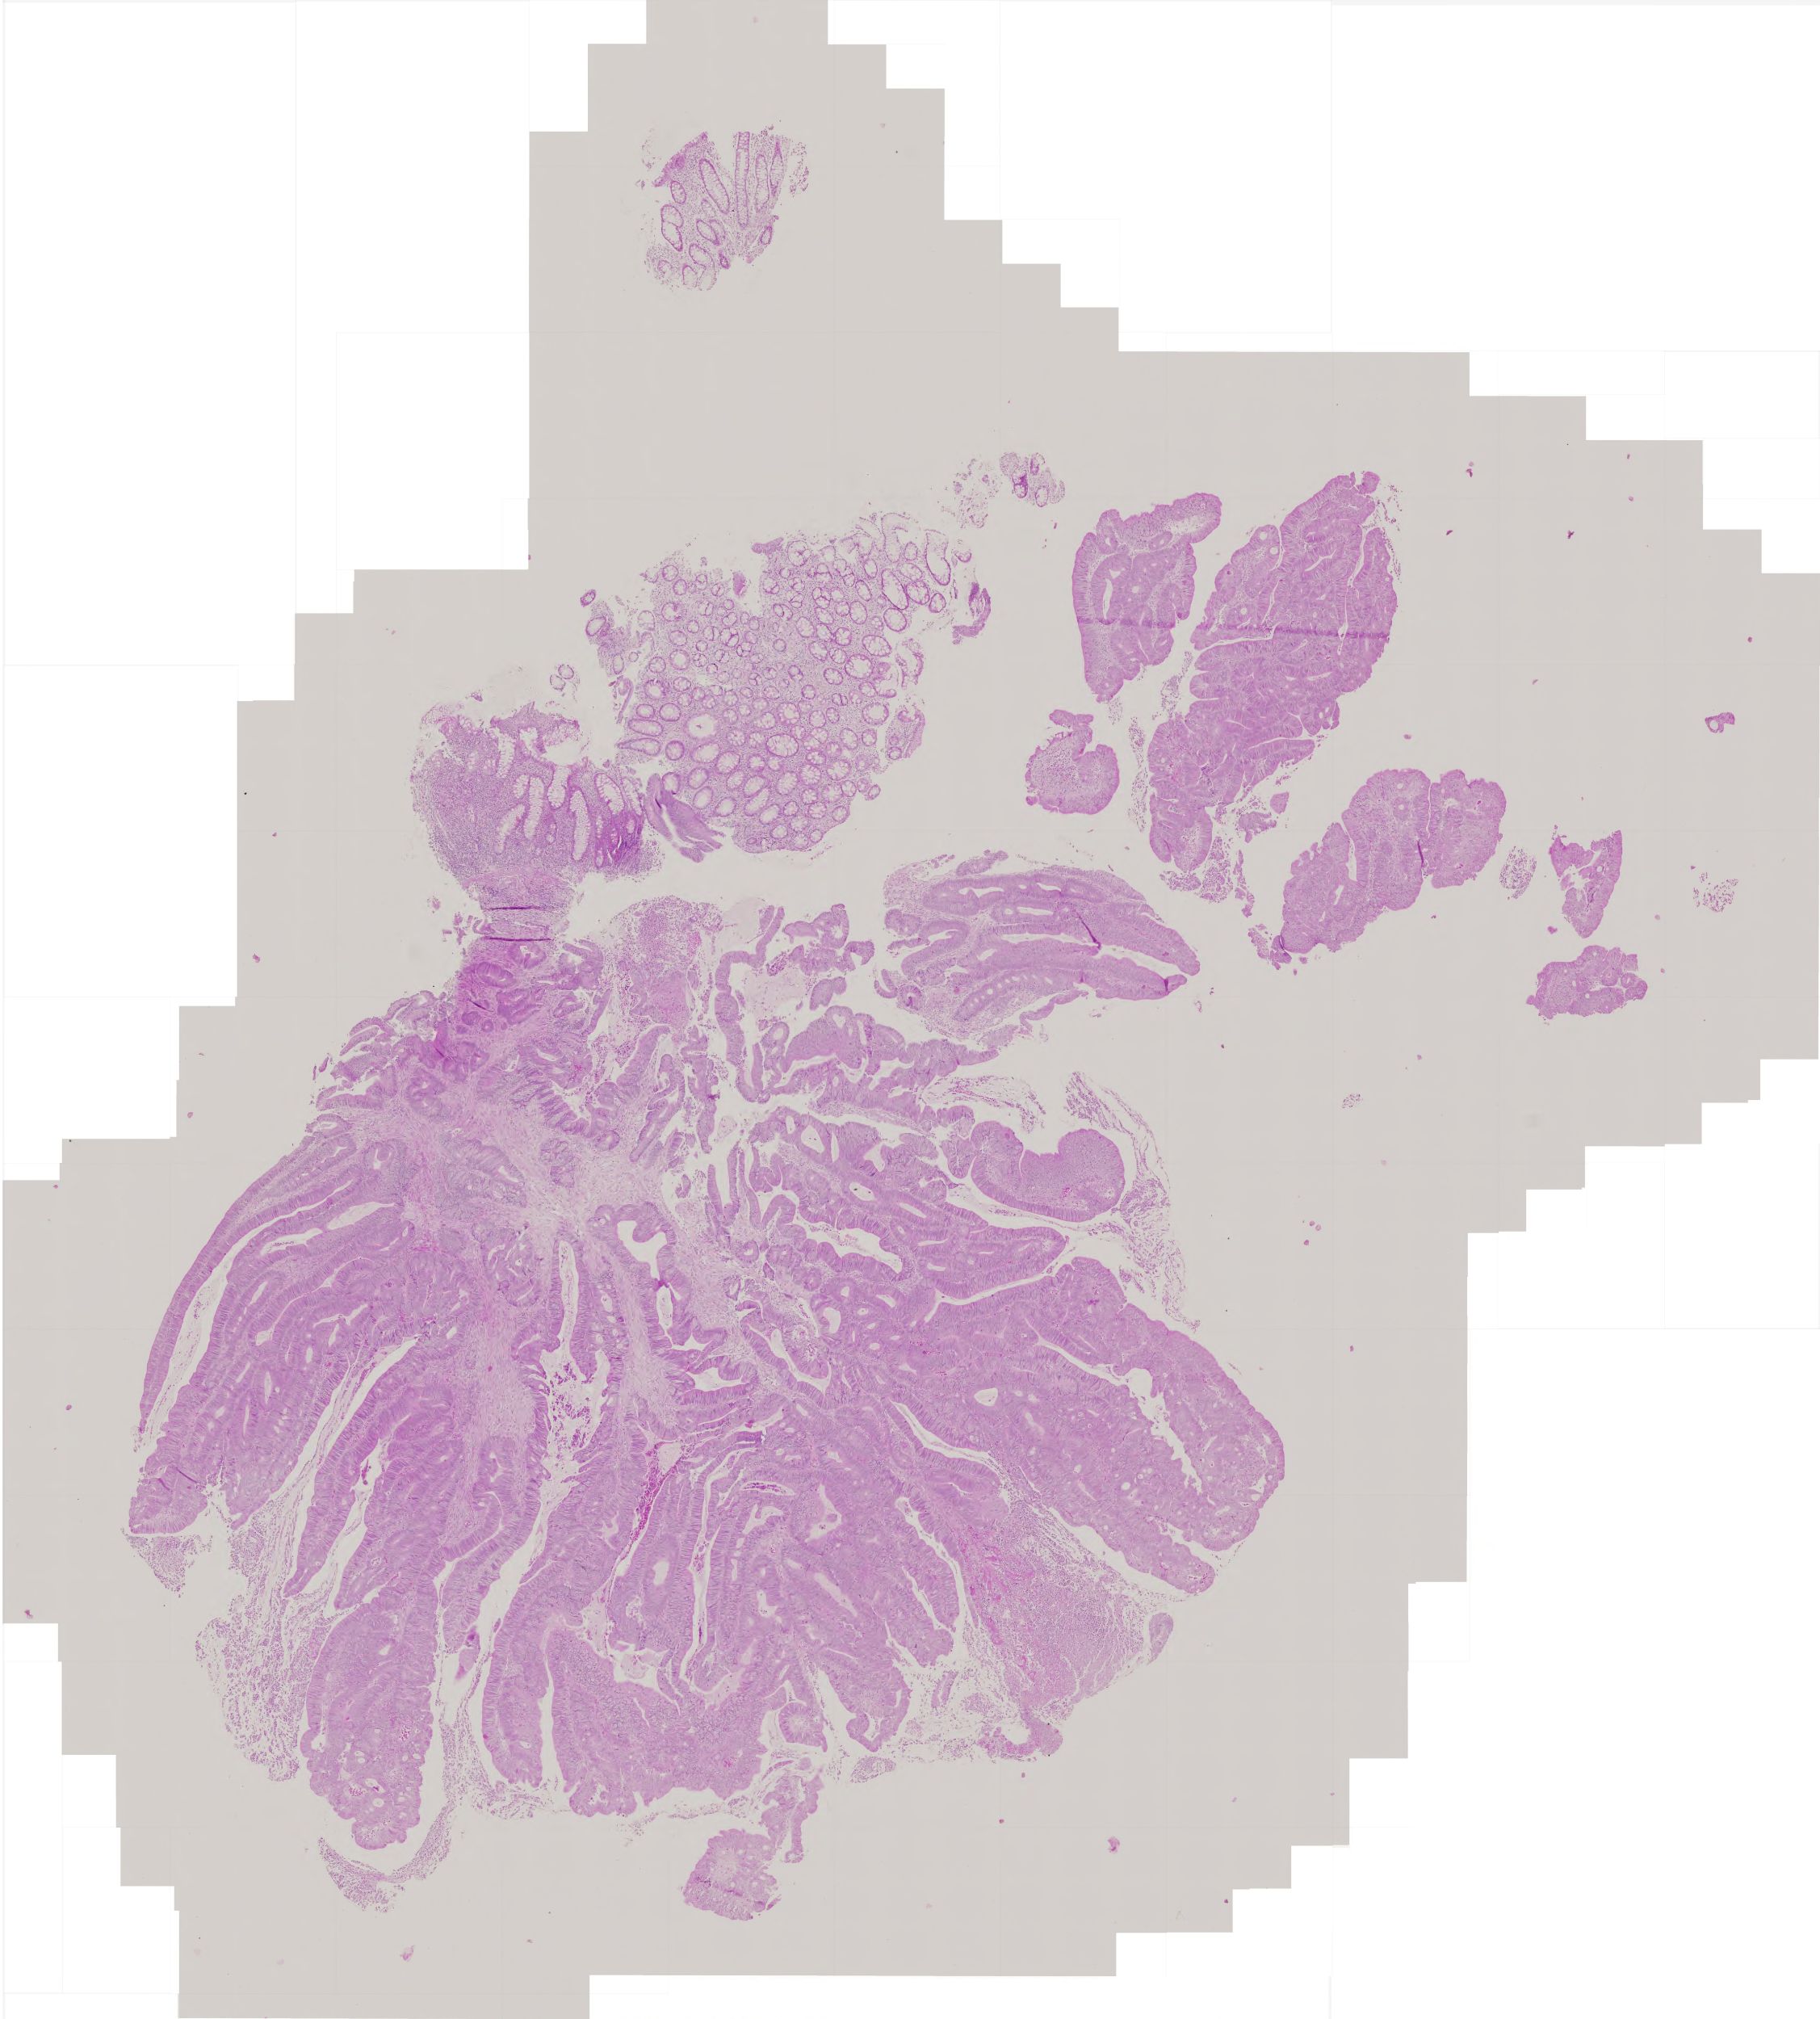
Digitized H&E tissue section (whole slide), low-resolution overview of the scanned area, about 4.5 x 5.0 mm; formalin-fixed paraffin-embedded (FFPE) diagnostic section; primary tumour sample from the colon. Female patient.
* diagnosis: Adenocarcinoma, NOS (ascending colon)
* lymph nodes positive (case pathology): 0 of 21 examined
* TNM: T3 N0 M0
* AJCC pathologic stage: II (5th edition)